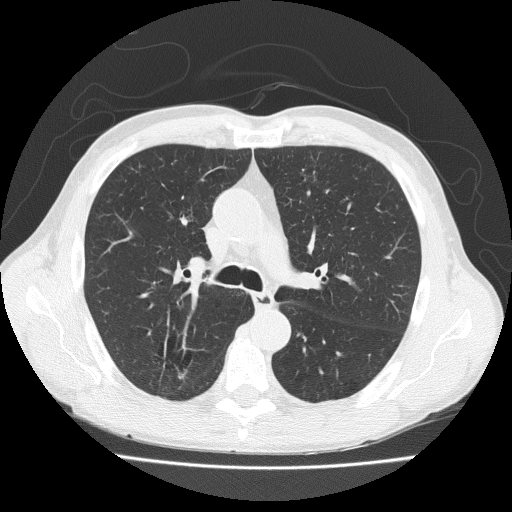
Axial slice from a low-dose chest CT screening exam, first (baseline) screen, lung window (W 1500 / L -600 HU), 2 mm slice thickness, slice 72 of 203 in the series. Male participant, aged 73 years at enrolment. Current smoker at enrolment.
Lesion marked by an expert reader, box from (x=144, y=335) to (x=195, y=382) px. No non-calcified nodule or mass ≥4 mm was recorded by the screening reader at this exam. Lung cancer was diagnosed 777 days after this screen (after the third annual screen): adenosquamous carcinoma, right upper lobe, well differentiated (G1), stage IA (AJCC 6th edition), 20 mm at pathology.